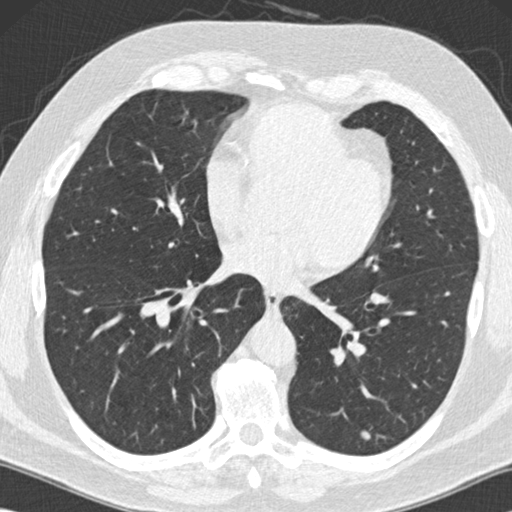
Low-dose screening chest CT, one axial slice; position 61 of 152 along the scan axis; reconstruction kernel B30f; 120 kVp; lung window (W 1500 / L -600 HU); 2 mm slice thickness; 512 × 512 image matrix.
Outlined on this slice (expert manual segmentation):
- lesion 1 (tumor, lower lobe of left lung): bounding box (x1, y1, x2, y2) in pixels: (361, 431, 370, 440)